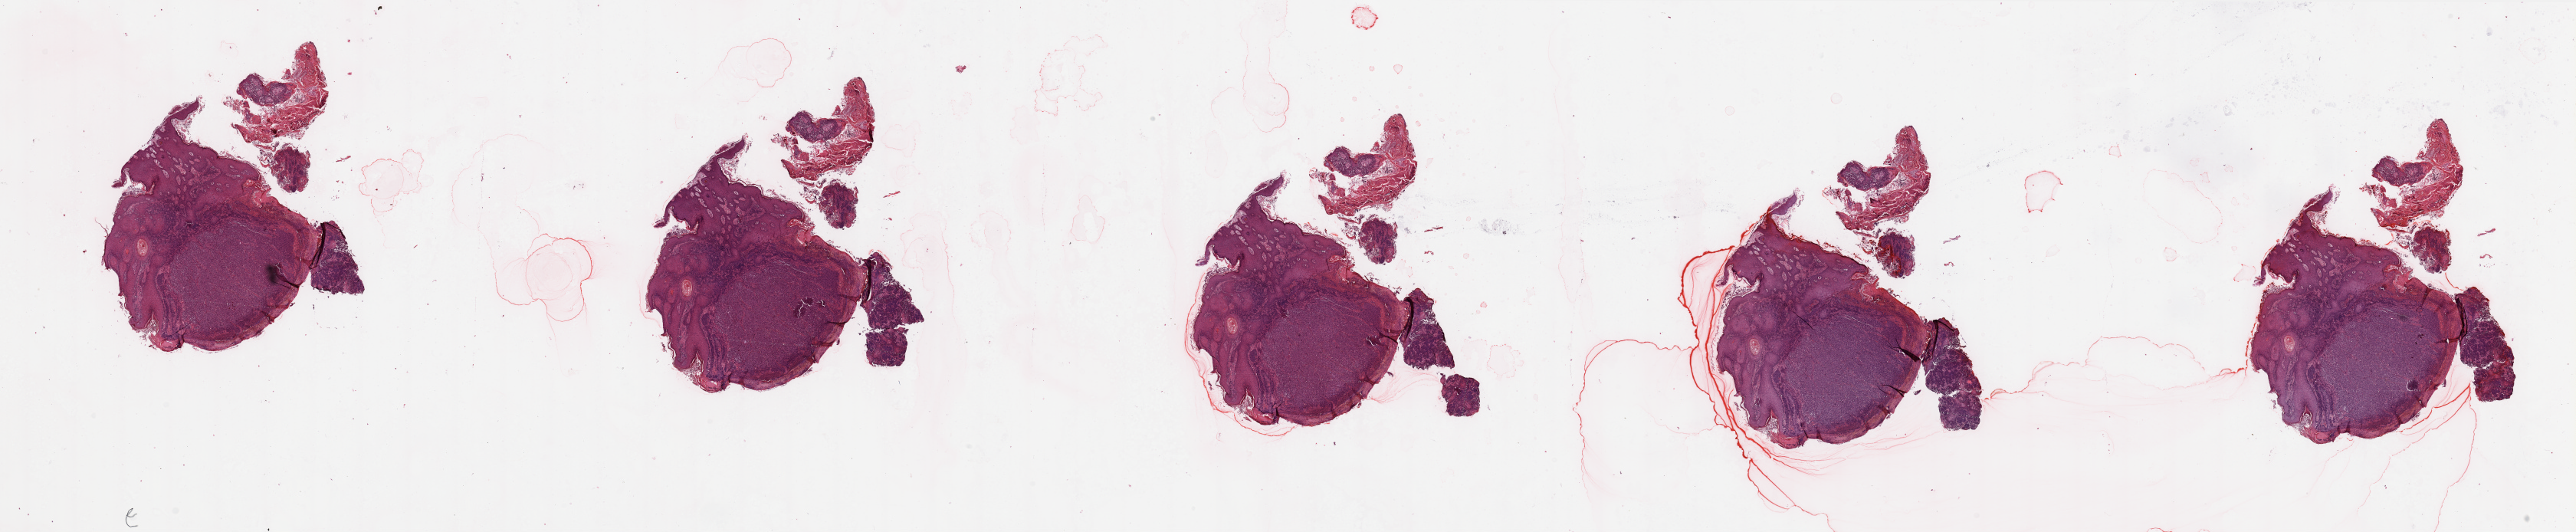
Digitized H&E-stained tissue section (whole slide) — low-resolution overview of the scanned area, about 53.2 x 11.0 mm (from a 20x scan). Melanoma tumour tissue; sampled site not recorded. Patient: male, age 42 years.
* histologic diagnosis: Malignant melanoma, NOS
* AJCC pathologic stage: IIC
* primary tumour site (as recorded): trunk